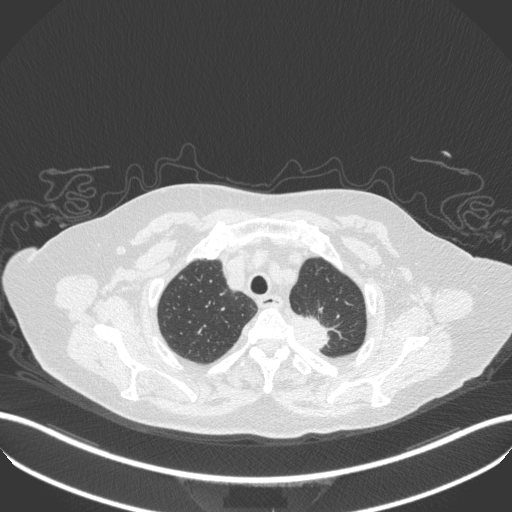
Chest CT, one axial slice; position 292 of 353 along the scan axis; reconstruction kernel B31f; 100 kVp; lung window (W 1500 / L -600 HU); 1 mm slice thickness; 512 × 512 image matrix, field of view 400 × 400 mm. Patient: female, 81 years. From the clinical record (not read from this slice): clinical TNM (as recorded): T2a N0 M0.
Structures marked on this image (rectangle marked by the reading radiologist):
- lung tumour (recorded histology: adenocarcinoma): bounding box <280,306,342,353> (left, top, right, bottom; pixels)